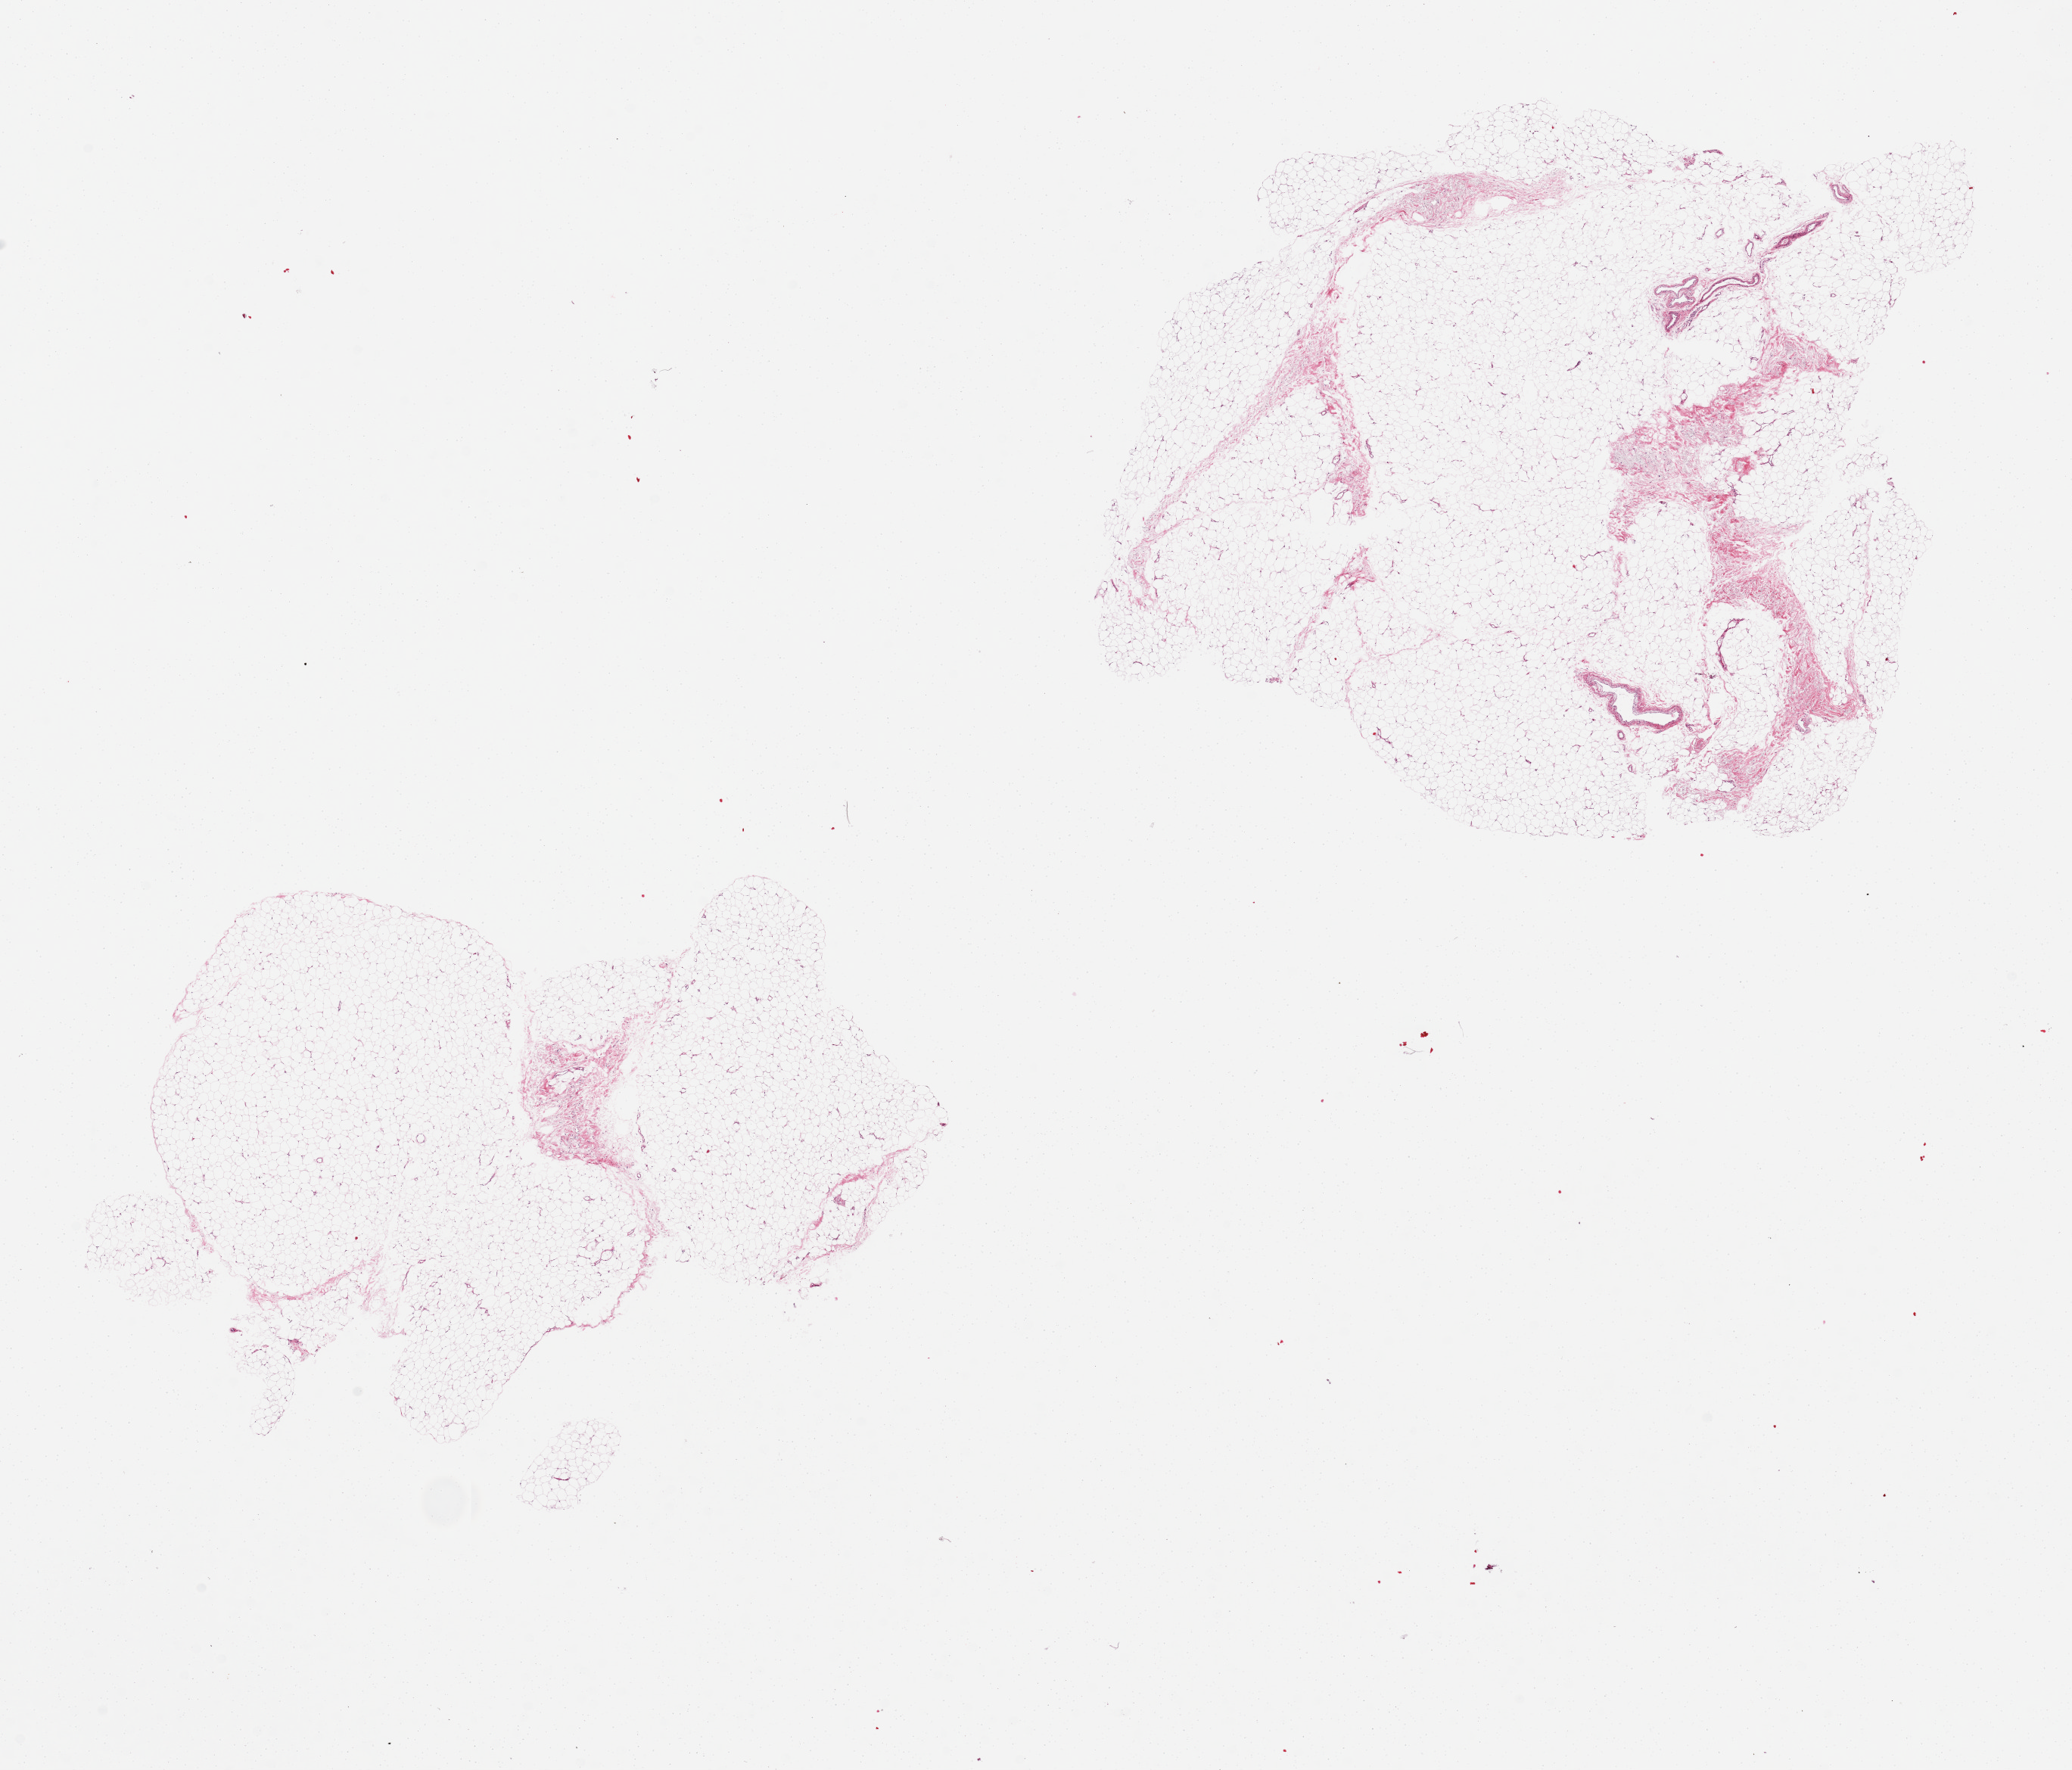
Digitized haematoxylin and eosin-stained section, brightfield — whole scanned area (about 21.7 x 18.5 mm) shown as a low-resolution overview. PAXgene-fixed paraffin-embedded (PFPE) section. Sampled site (target tissue): adipose tissue. Tissue donor sample. Female donor.
• pathologist's review note for this sample: 2 pieces, ~10% fibrous tissue/vessel